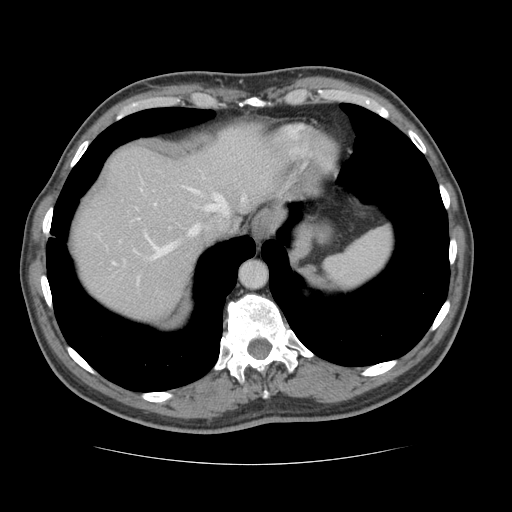
Contrast-enhanced abdominal CT, one axial slice; slice 111 of 134 in the series (ordered by position); reconstruction kernel STANDARD; 120 kVp; intravenous contrast given; soft-tissue window (W 400 / L 40 HU); 512 × 512 image matrix, field of view 377 × 377 mm. Male patient, age 68 years. From the clinical record (not read from this slice): diagnosis: colorectal cancer liver metastases, imaged before liver resection; multiple liver metastases: yes; largest metastasis: 2.2 cm.
Structures marked on this image (manually delineated by an expert):
- hepatic veins: box from (x=113, y=185) to (x=246, y=264) px
- liver: (x=73, y=131)–(x=275, y=317)
- planned liver remnant (the part of the liver to remain after resection): (x=73, y=129)–(x=276, y=307)